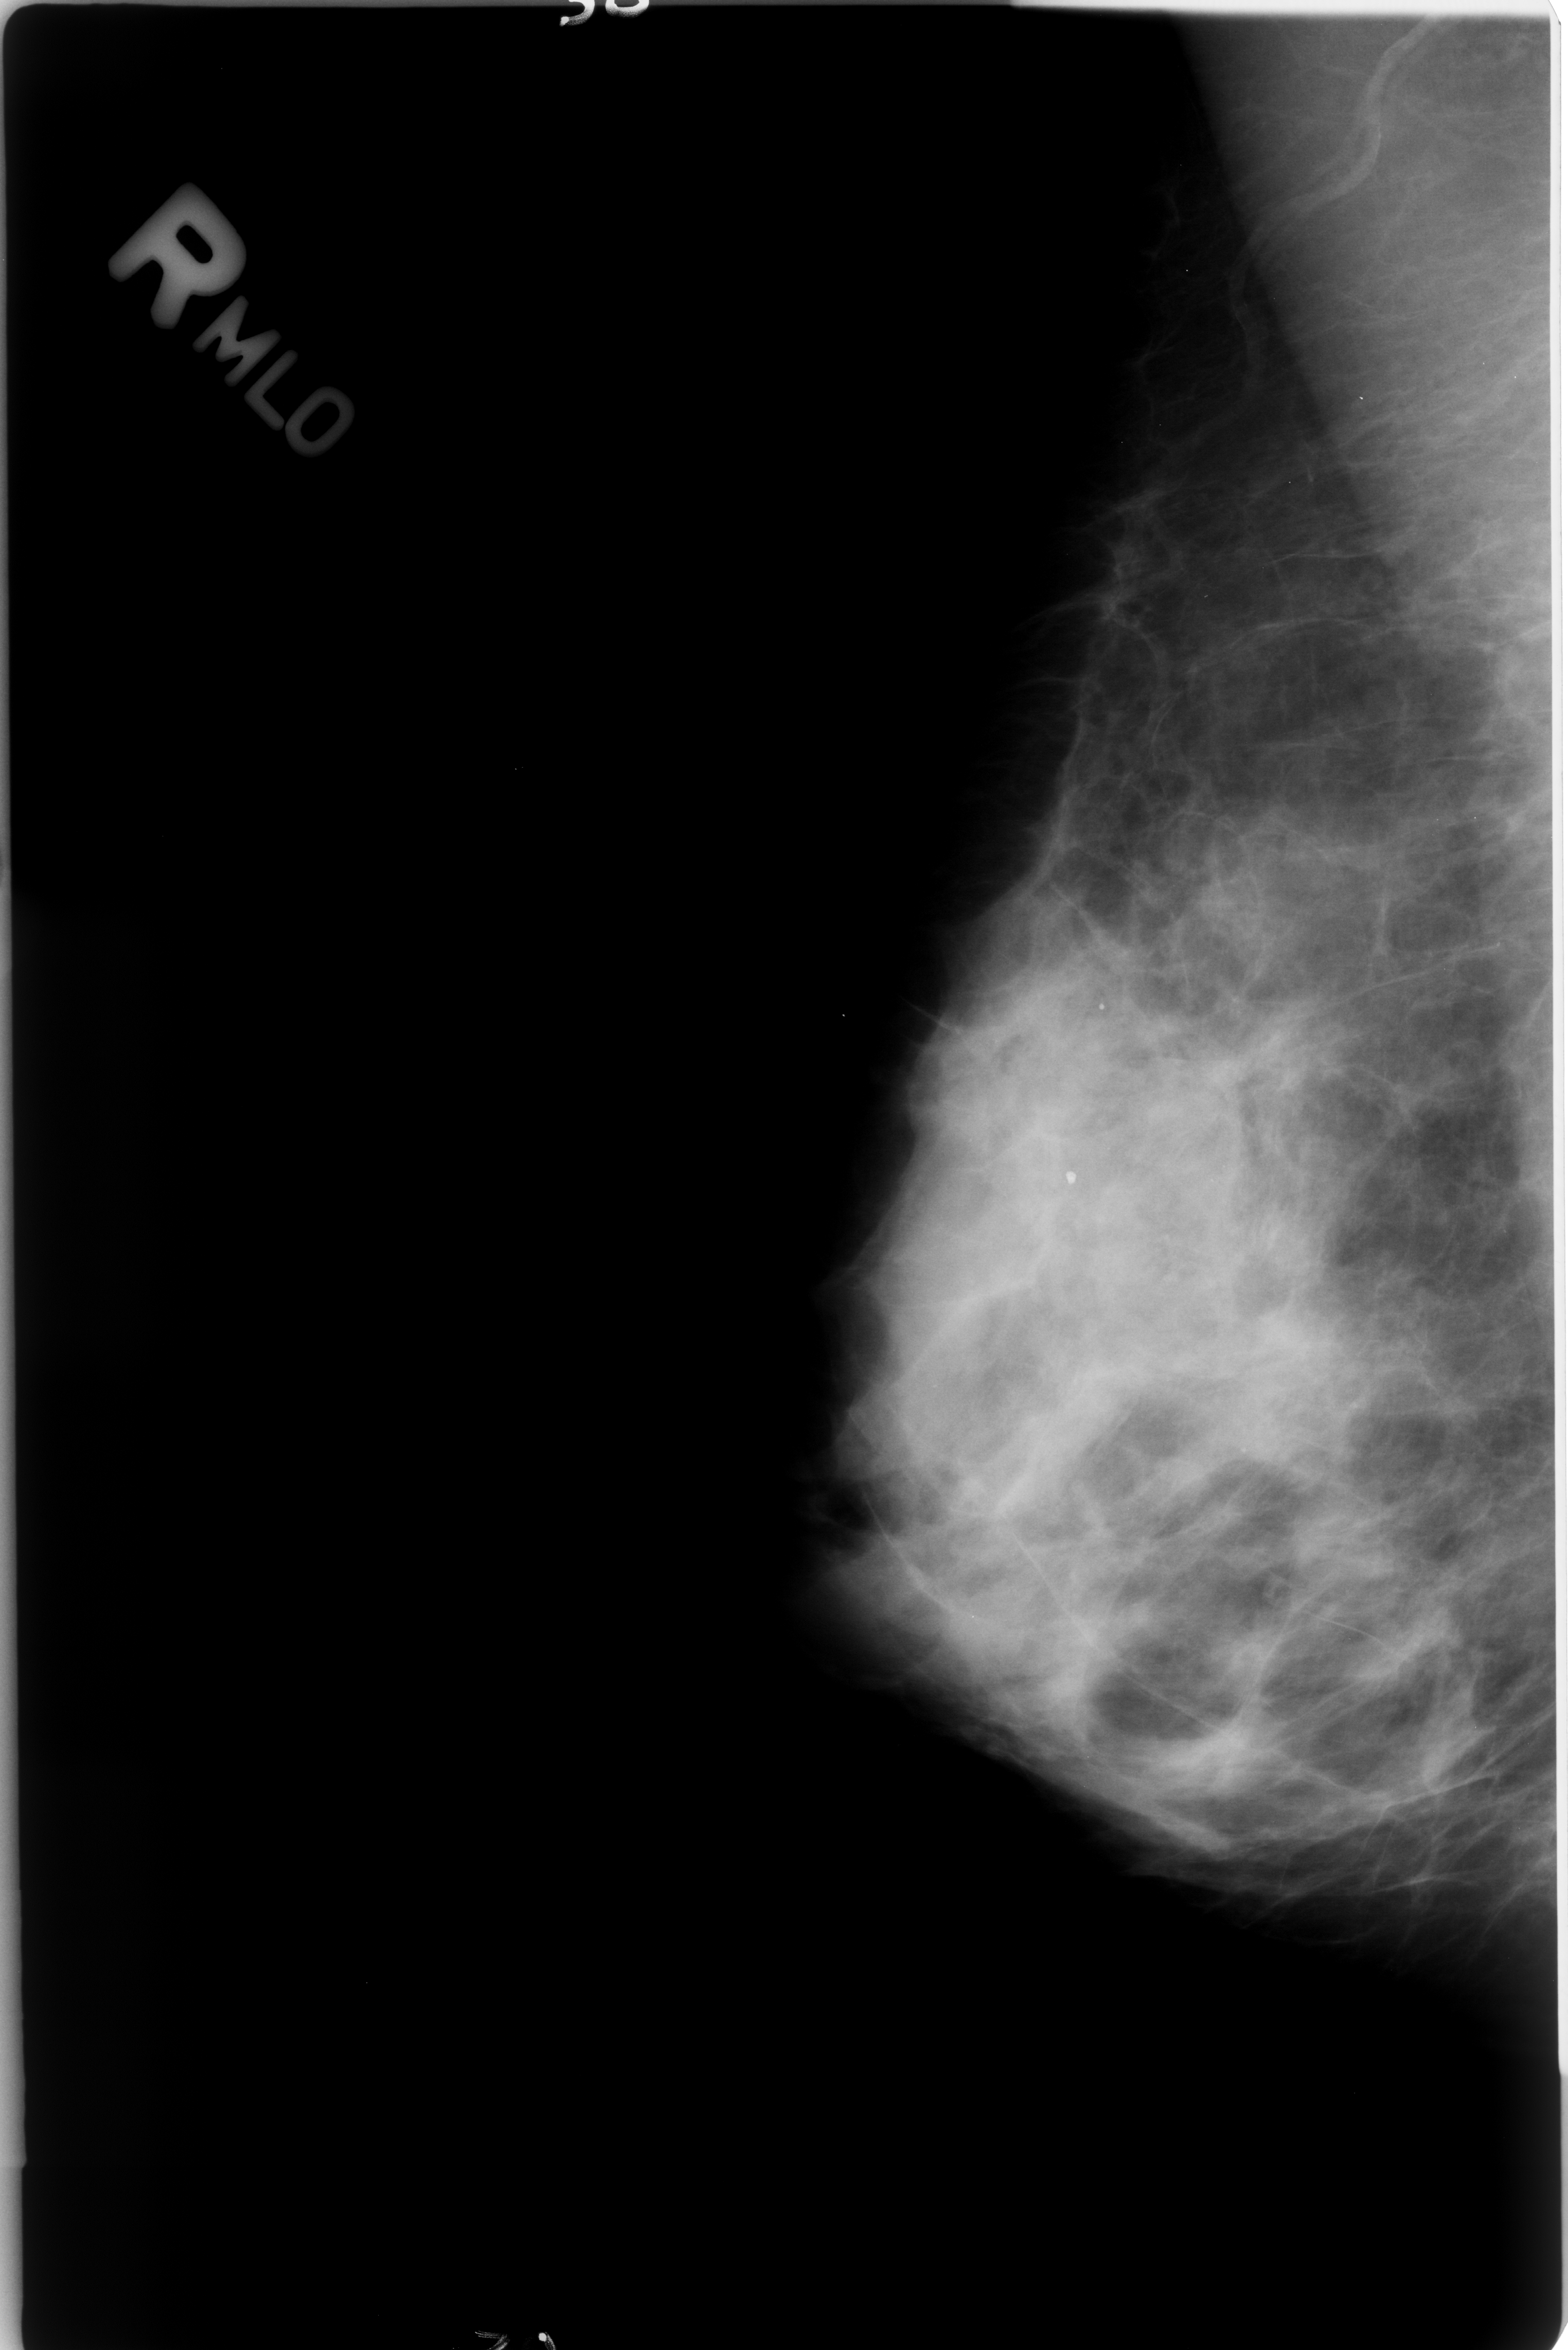
Mammogram (digitized film), right breast, MLO view, BI-RADS breast density category 3 (scale 1–4).
Marked findings (only marked abnormalities are described; nothing is implied about the rest of the image): Finding 1 of 2: calcifications, morphology round and regular / lucent center; BI-RADS assessment category 2; subtlety rating 4 on a 1 (subtle) to 5 (obvious) scale; benign; no additional work-up was recommended (benign without callback). Finding 2 of 2: calcifications, morphology round and regular / lucent center; BI-RADS assessment category 2; subtlety rating 4 on a 1 (subtle) to 5 (obvious) scale; benign; no additional work-up was recommended (benign without callback).